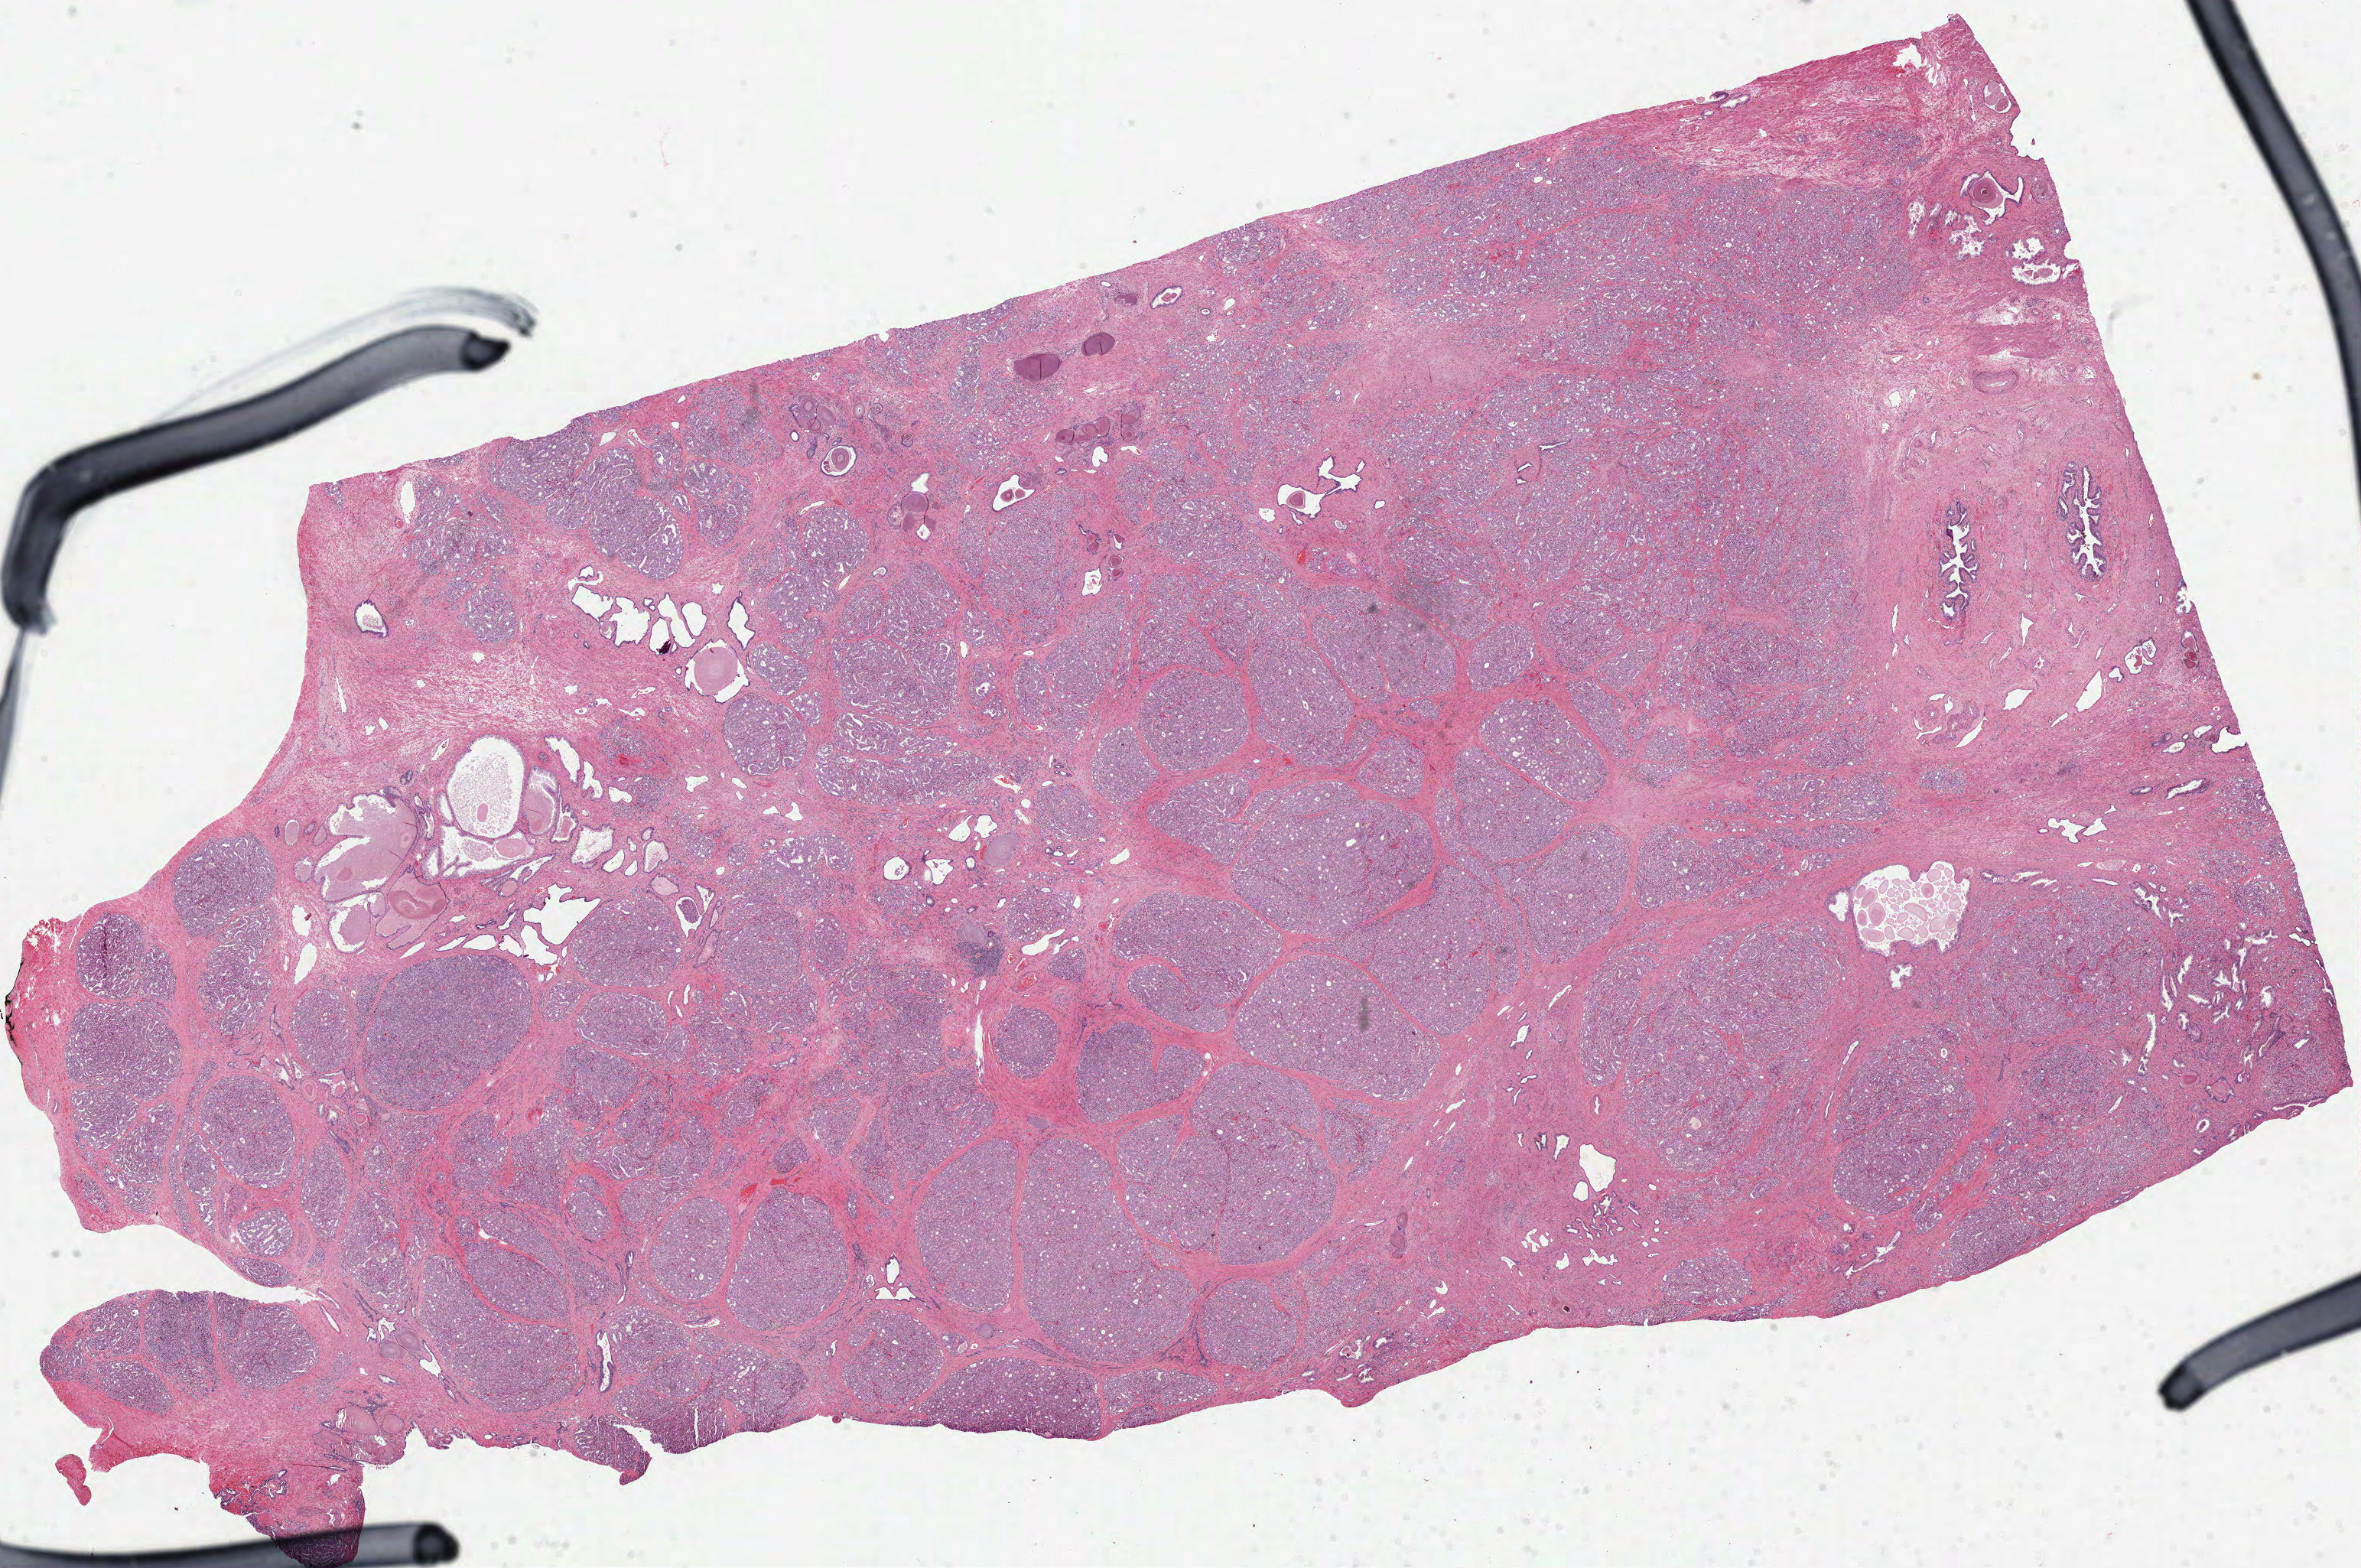
H&E-stained whole-slide image — low-resolution overview of the scanned area, about 24.9 x 16.5 mm (from a 40x scan), formalin-fixed paraffin-embedded (FFPE) diagnostic section, primary tumour sample from the prostate. Male, age 64 years at initial diagnosis. Gleason score: 8 (4+4).
Histologic diagnosis: Acinar cell carcinoma (prostate gland). Laterality: bilateral. Lymph nodes positive (case pathology): 3 of 12 examined.